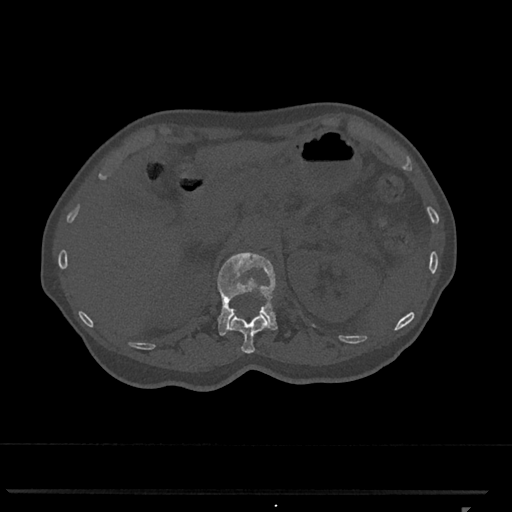
CT including the spine, one axial slice; position 430 of 793 along the scan axis; bone window (W 1800 / L 400 HU); 512 × 512 image matrix, field of view 380 × 380 mm. Female patient, age 62 years. From the clinical record (not read from this slice): primary cancer: renal.
Outlined on this slice (semi-automatic segmentation, software-assisted and operator-edited):
- L1 vertebra: bounding box [x1, y1, x2, y2] px = [217, 252, 278, 336]
- T12 vertebra: [229, 312, 268, 354]